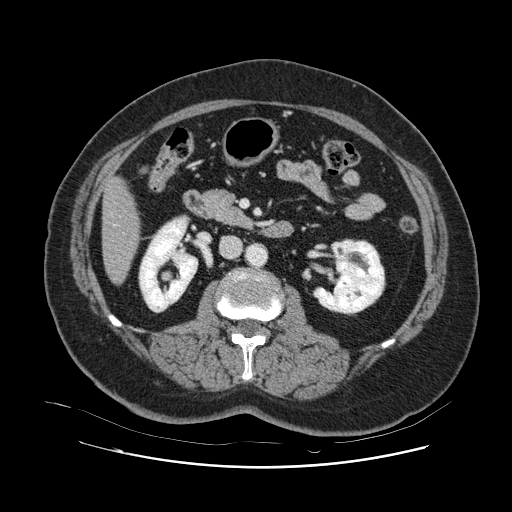
Contrast-enhanced abdominal CT, one axial slice. Position 29 of 132 along the scan axis. 120 kVp. Intravenous contrast given. Soft-tissue window (W 400 / L 40 HU). 2.5 mm slice thickness. 512 × 512 image matrix, field of view 391 × 391 mm. Female patient, age 73 years. Case-level facts recorded for this patient, not image findings: diagnosis: colorectal cancer liver metastases, imaged before liver resection; multiple liver metastases: no; largest metastasis: 7 cm; disease in both lobes: no.
Annotated regions visible in this slice (manually delineated by an expert):
- hepatic veins: bounding box <113,224,117,226> (left, top, right, bottom; pixels)
- liver: <103,181,139,282>
- planned liver remnant (the part of the liver to remain after resection): <103,181,139,283>